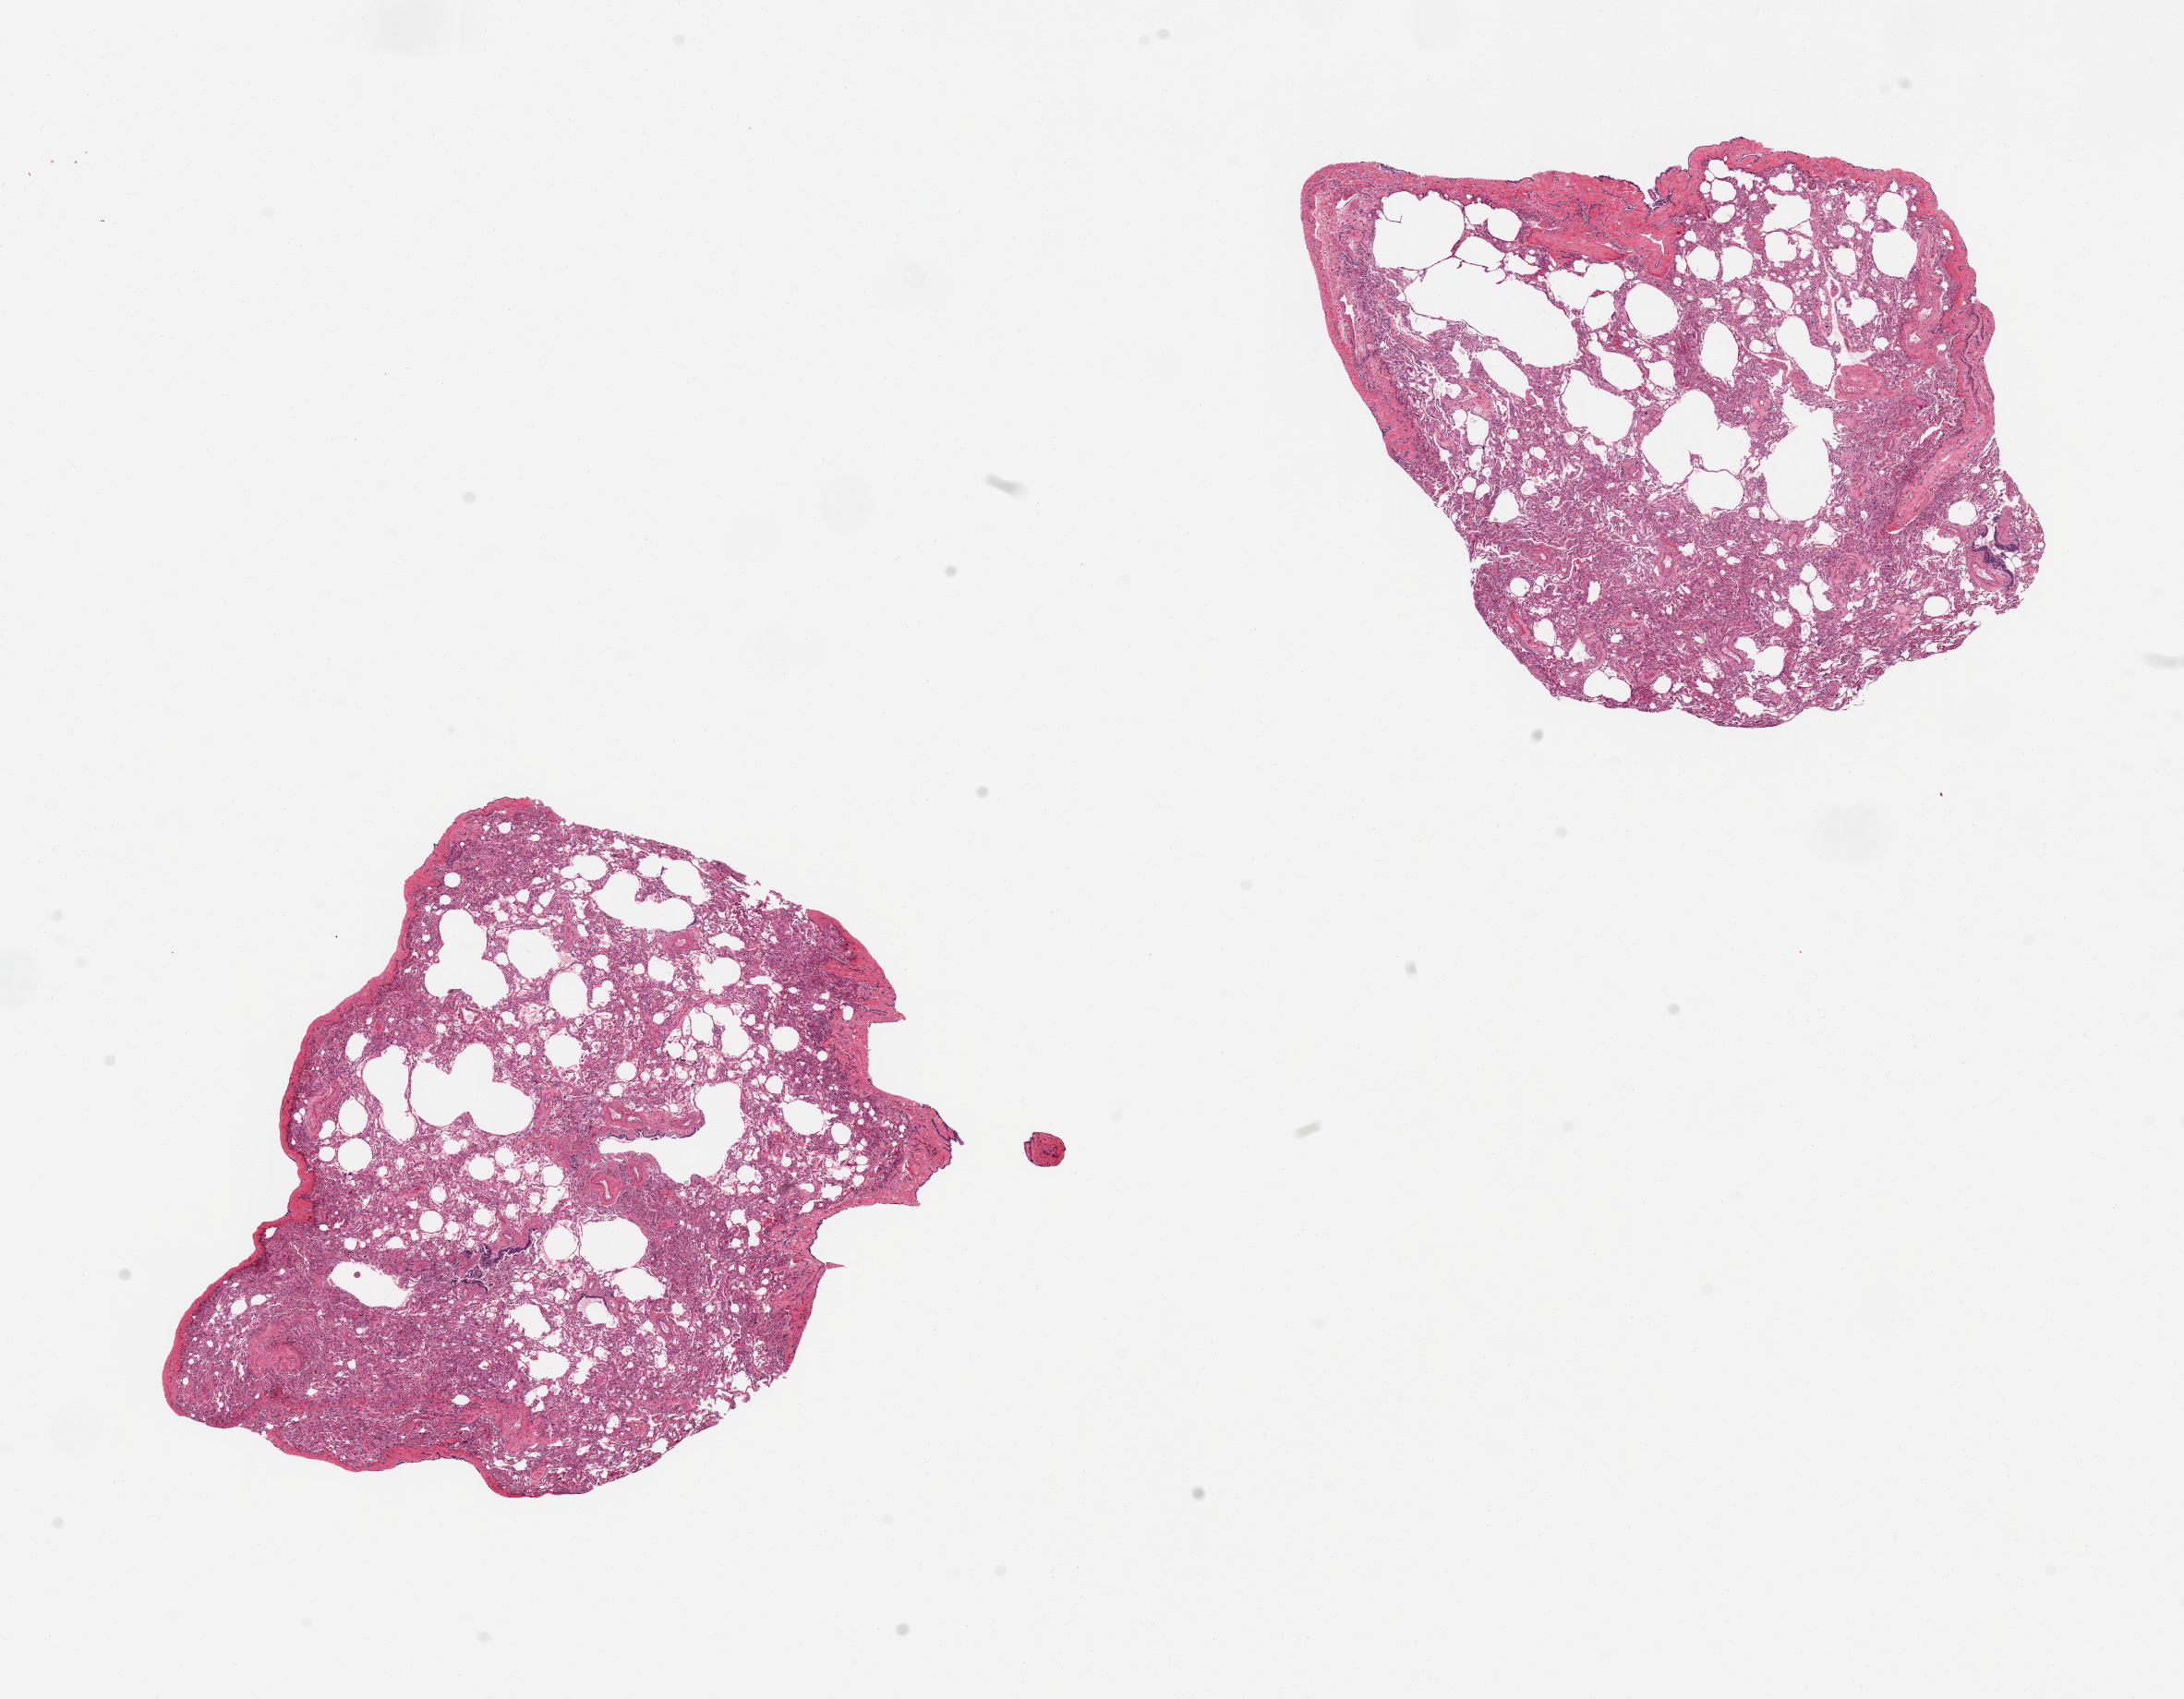
Digitized haematoxylin and eosin-stained section — low-resolution overview of the scanned area, about 18.7 x 14.6 mm; PAXgene-fixed paraffin-embedded (PFPE) section; sampled site (target tissue): lung; tissue donor sample. Female donor.
* review note (as recorded): 2 pieces, includes pleura (target is 1 cm below pleura), some fibrosis, atelectasis, and emphysematous change, scattered neutrophils